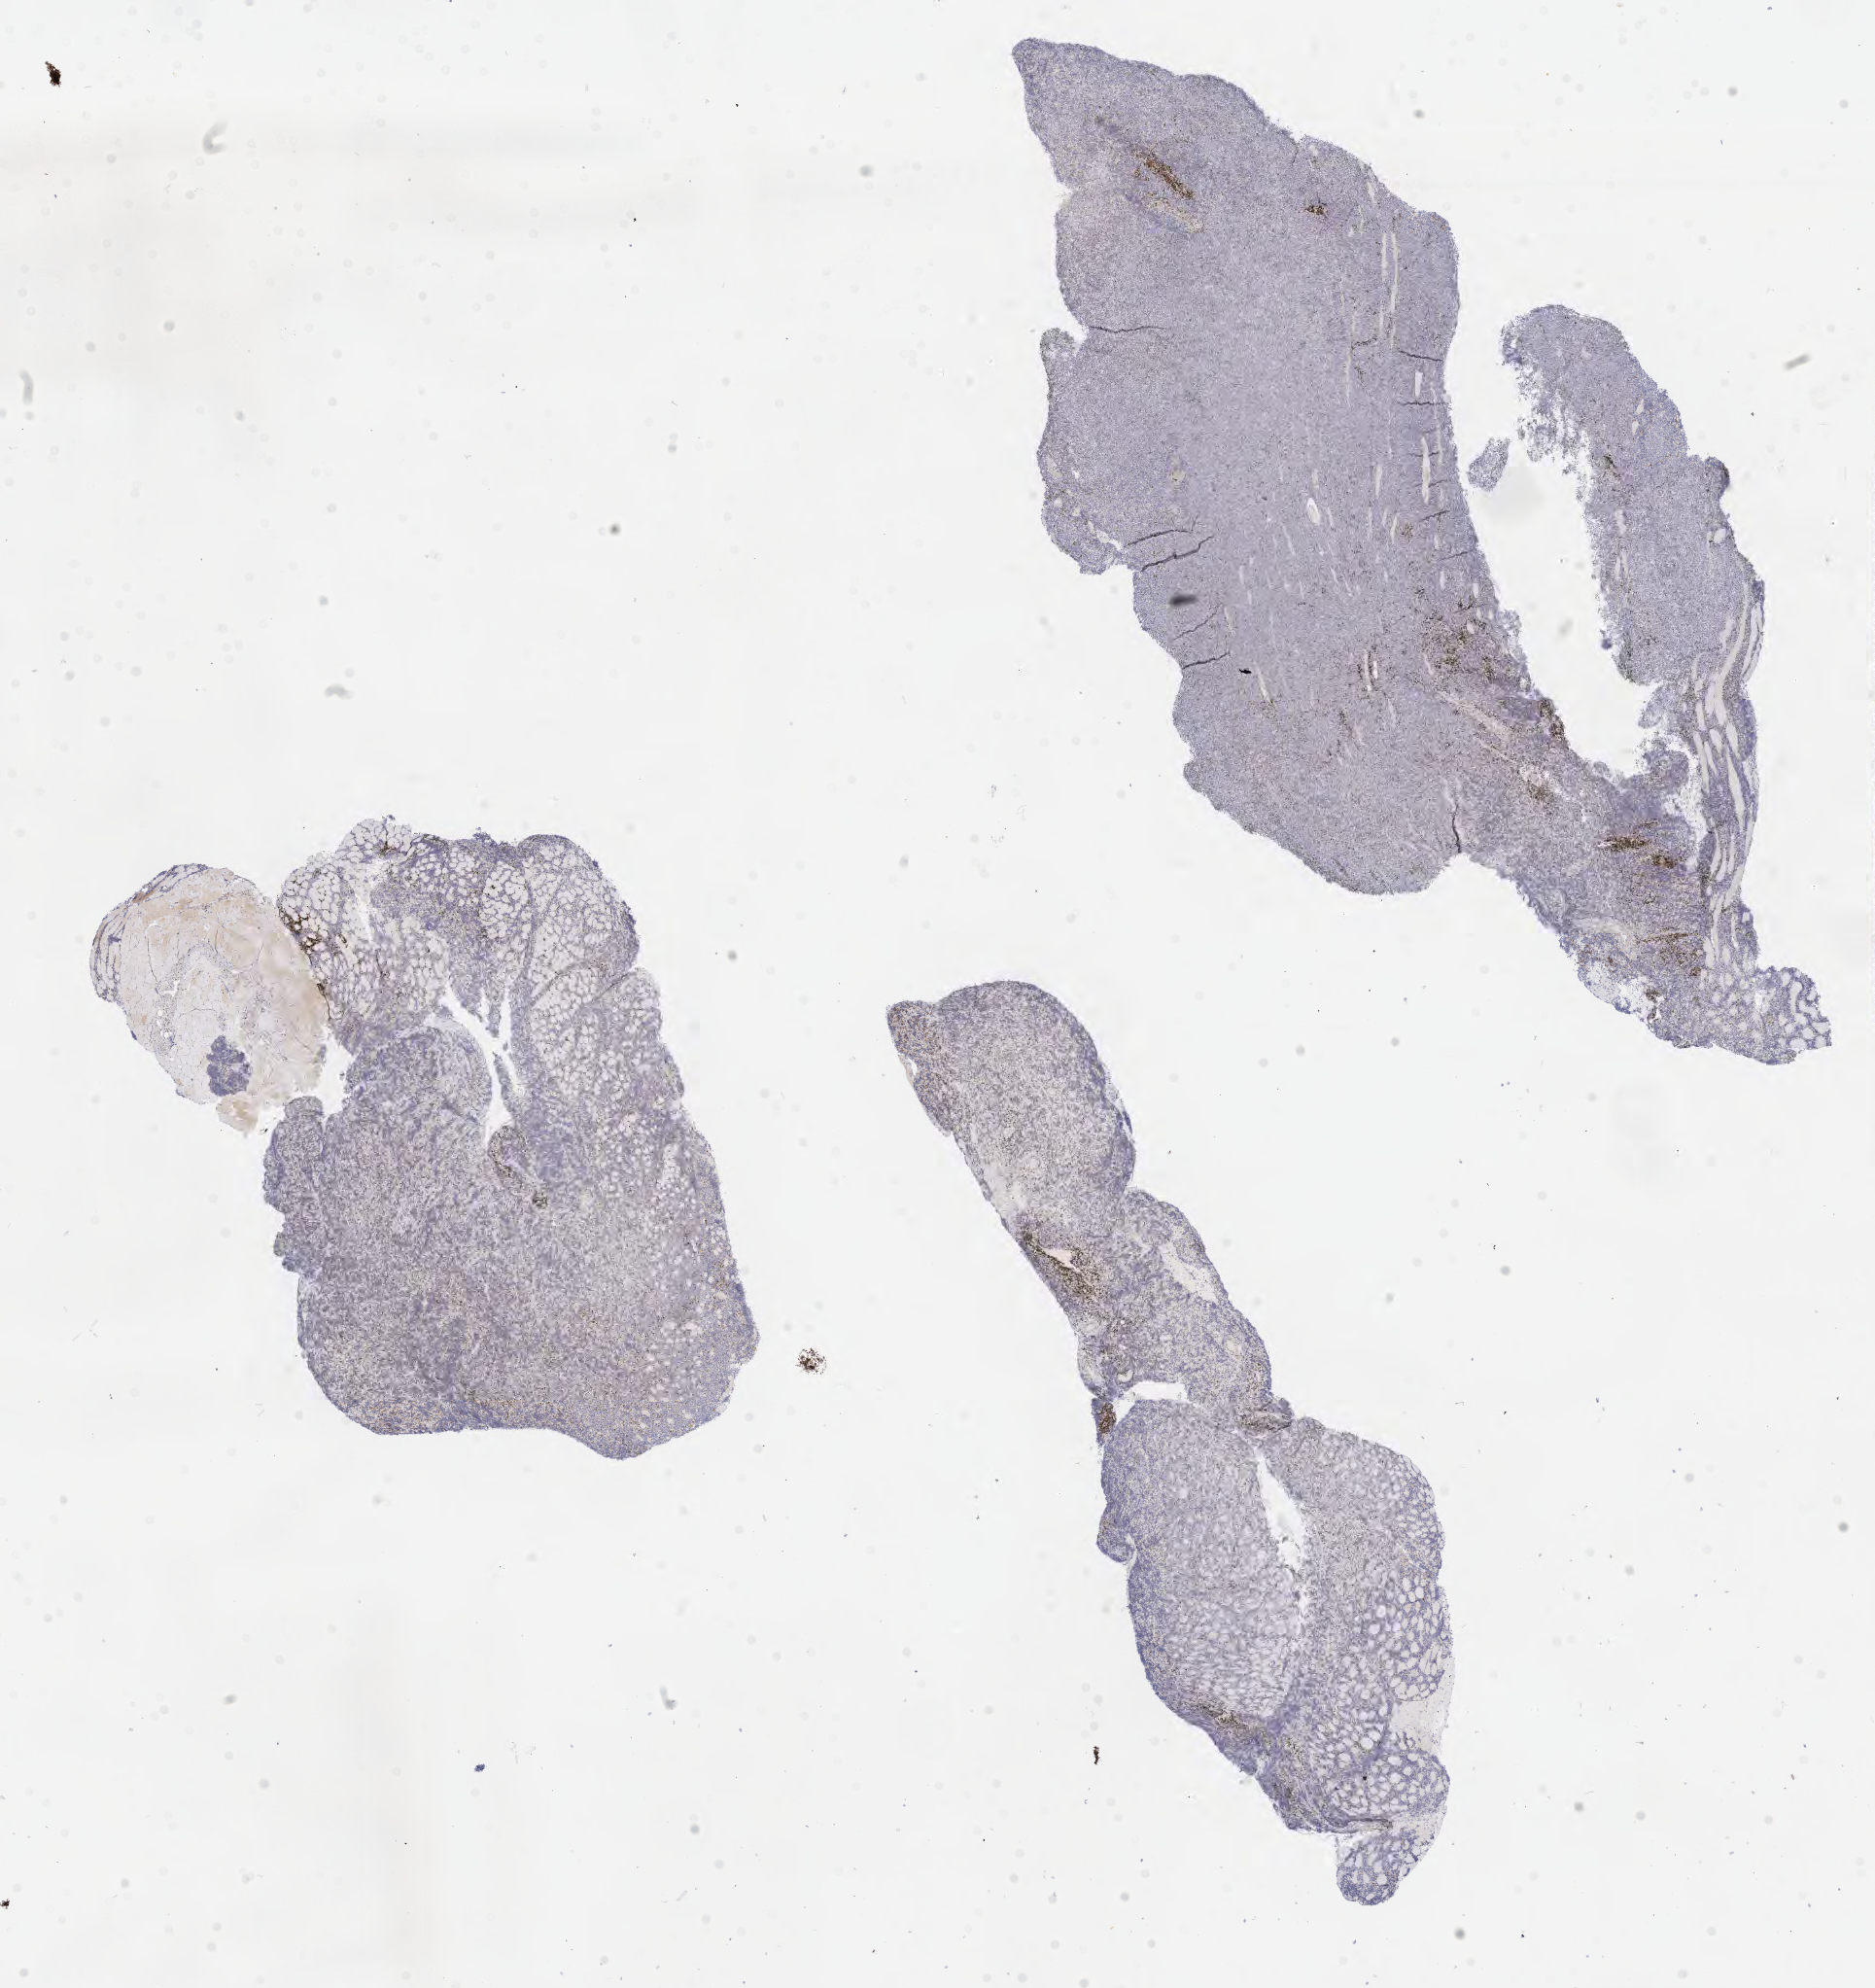
IHC for BCL2, whole-slide image, a low-resolution overview of the entire scanned area, about 15.6 x 16.5 mm, specimen: tumor tissue, anatomic site: lymph node of head and neck. Male patient, 55 years old.
* diagnosis: Burkitt lymphoma, NOS